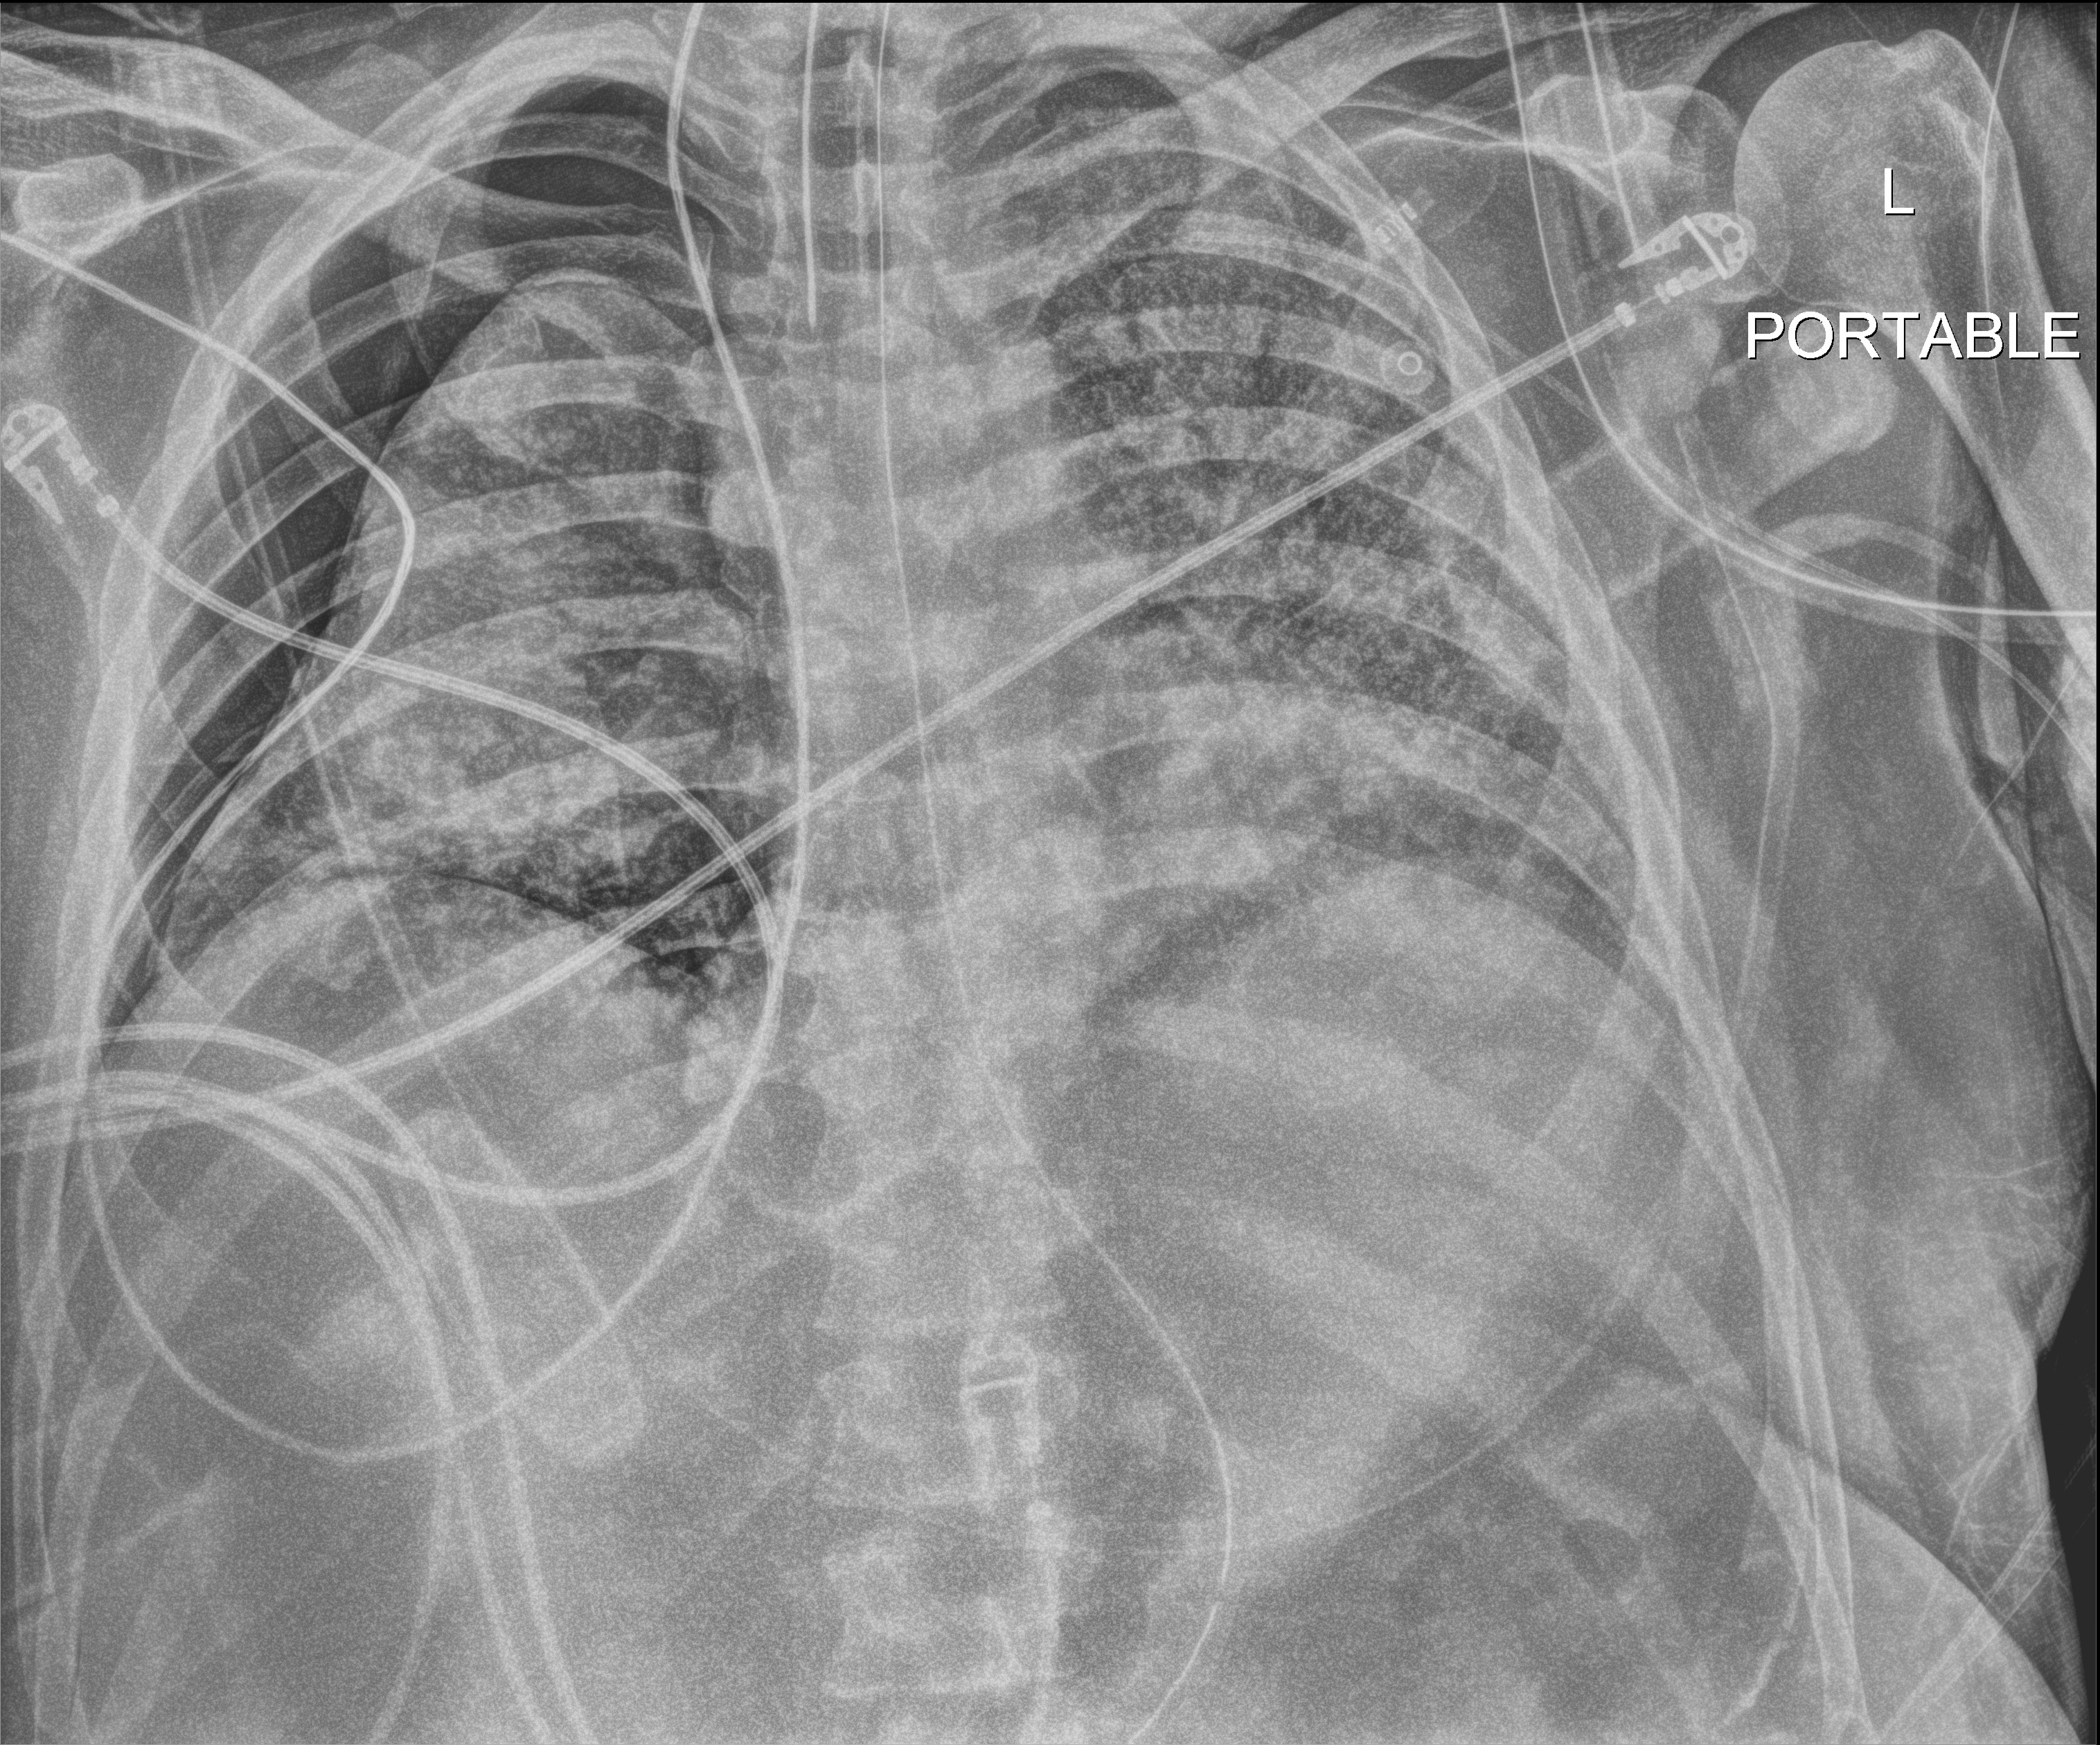
Bedside chest radiograph (digital radiography), anteroposterior (AP) projection. Male patient hospitalised with COVID-19, age 18–59 years.
Hospital-stay facts (about this admission, not read from this image; timing relative to this image not recorded): mechanically ventilated during this hospital stay: yes; admitted to intensive care during this hospital stay: yes.